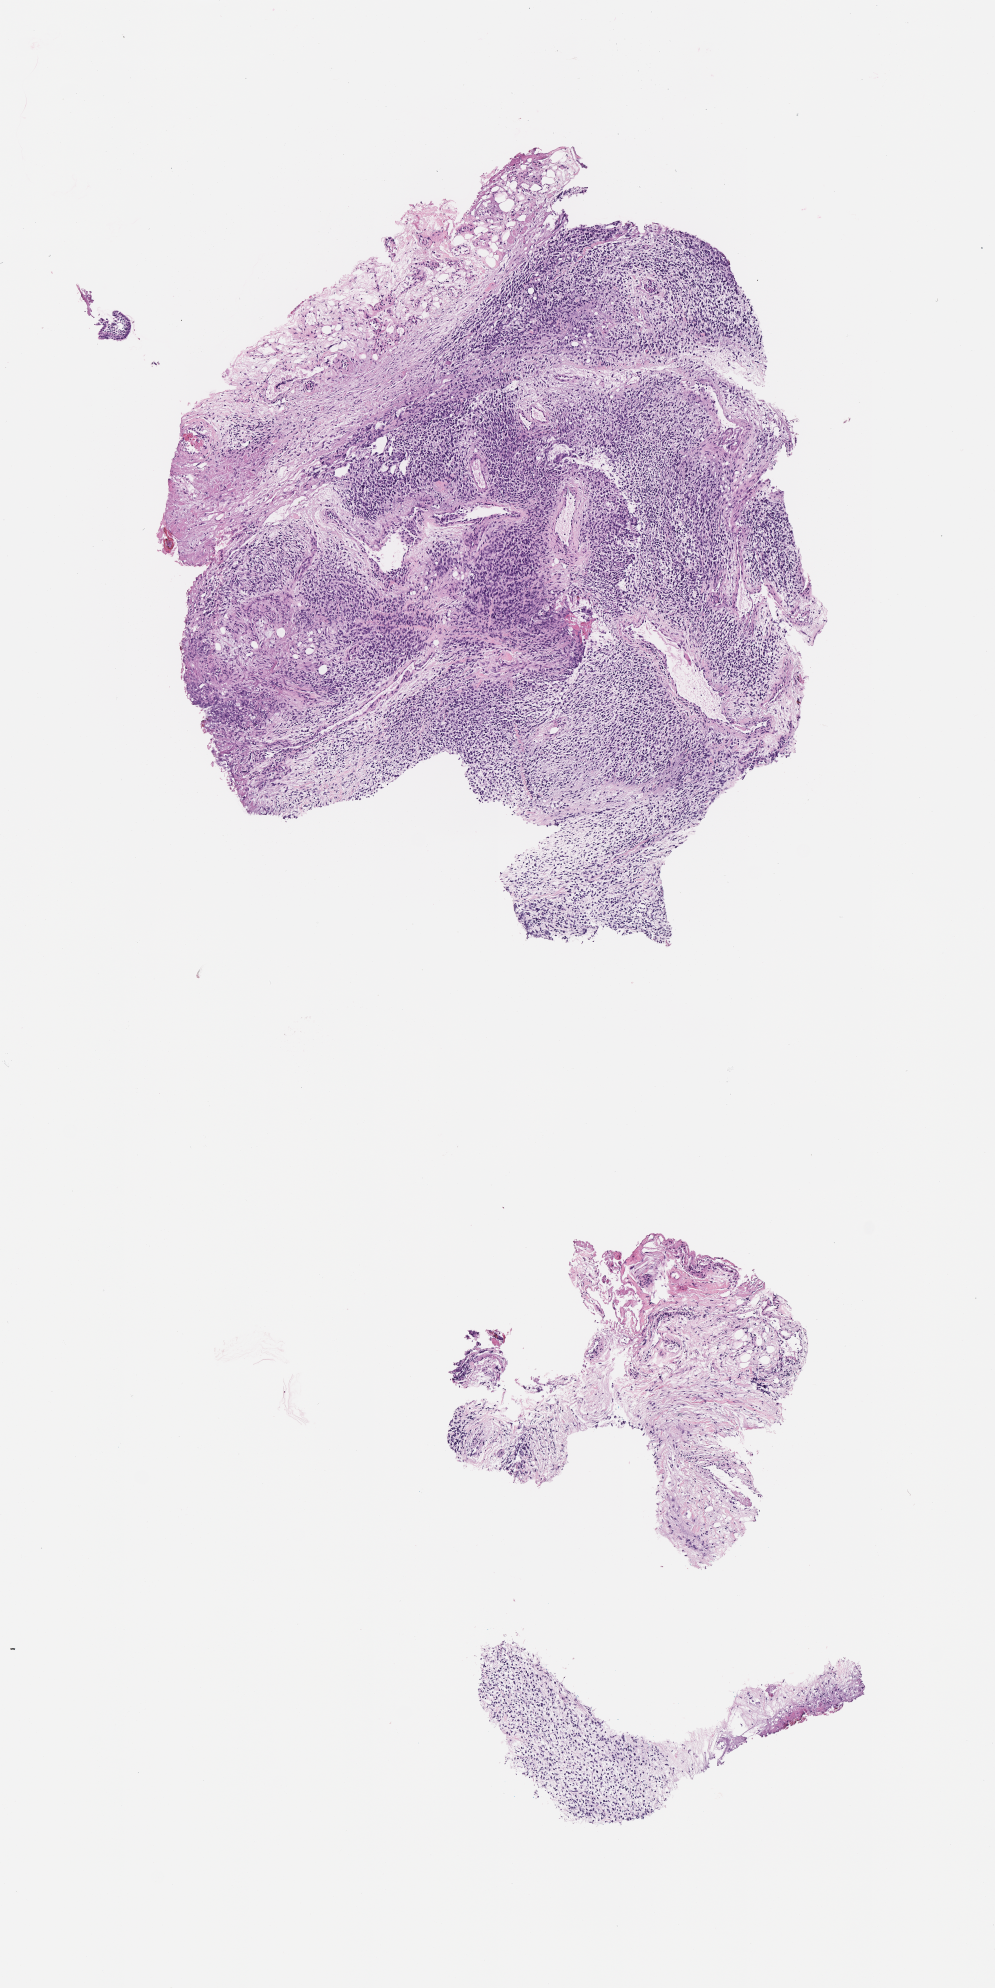
Whole-slide image, hematoxylin and eosin (H&E) stain of tumor tissue, a low-resolution overview of the entire scanned area, about 4.0 x 8.0 mm; formalin-fixed paraffin-embedded section. Male patient, age at diagnosis 8.3 years.
Stage (as recorded): 1. Diagnosis: rhabdomyosarcoma; histological classification: embryonal rhabdomyosarcoma. Metastatic status at presentation (as recorded): non-metastatic.